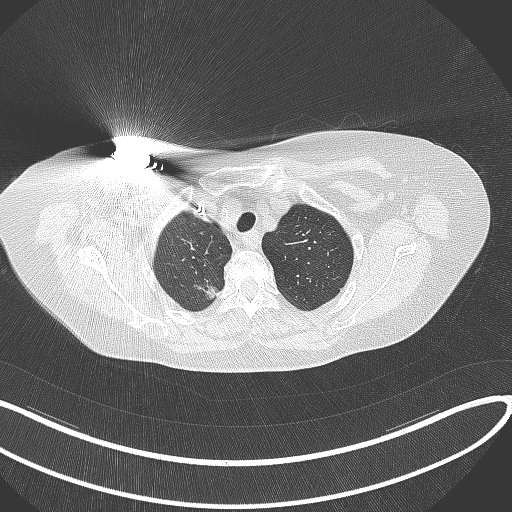
Chest CT, one axial slice. Position 284 of 316 along the scan axis. Reconstruction kernel B70f. 120 kVp. Lung window (W 1500 / L -600 HU). 1 mm slice thickness. 512 × 512 image matrix, field of view 400 × 400 mm. Female patient, age 72 years. From the clinical record (not read from this slice): clinical TNM (as recorded): T1c N0 M0.
Structures marked on this image (bounding box drawn by a radiologist):
- lung tumour (recorded histology: adenocarcinoma): box from (x=194, y=277) to (x=219, y=300) px